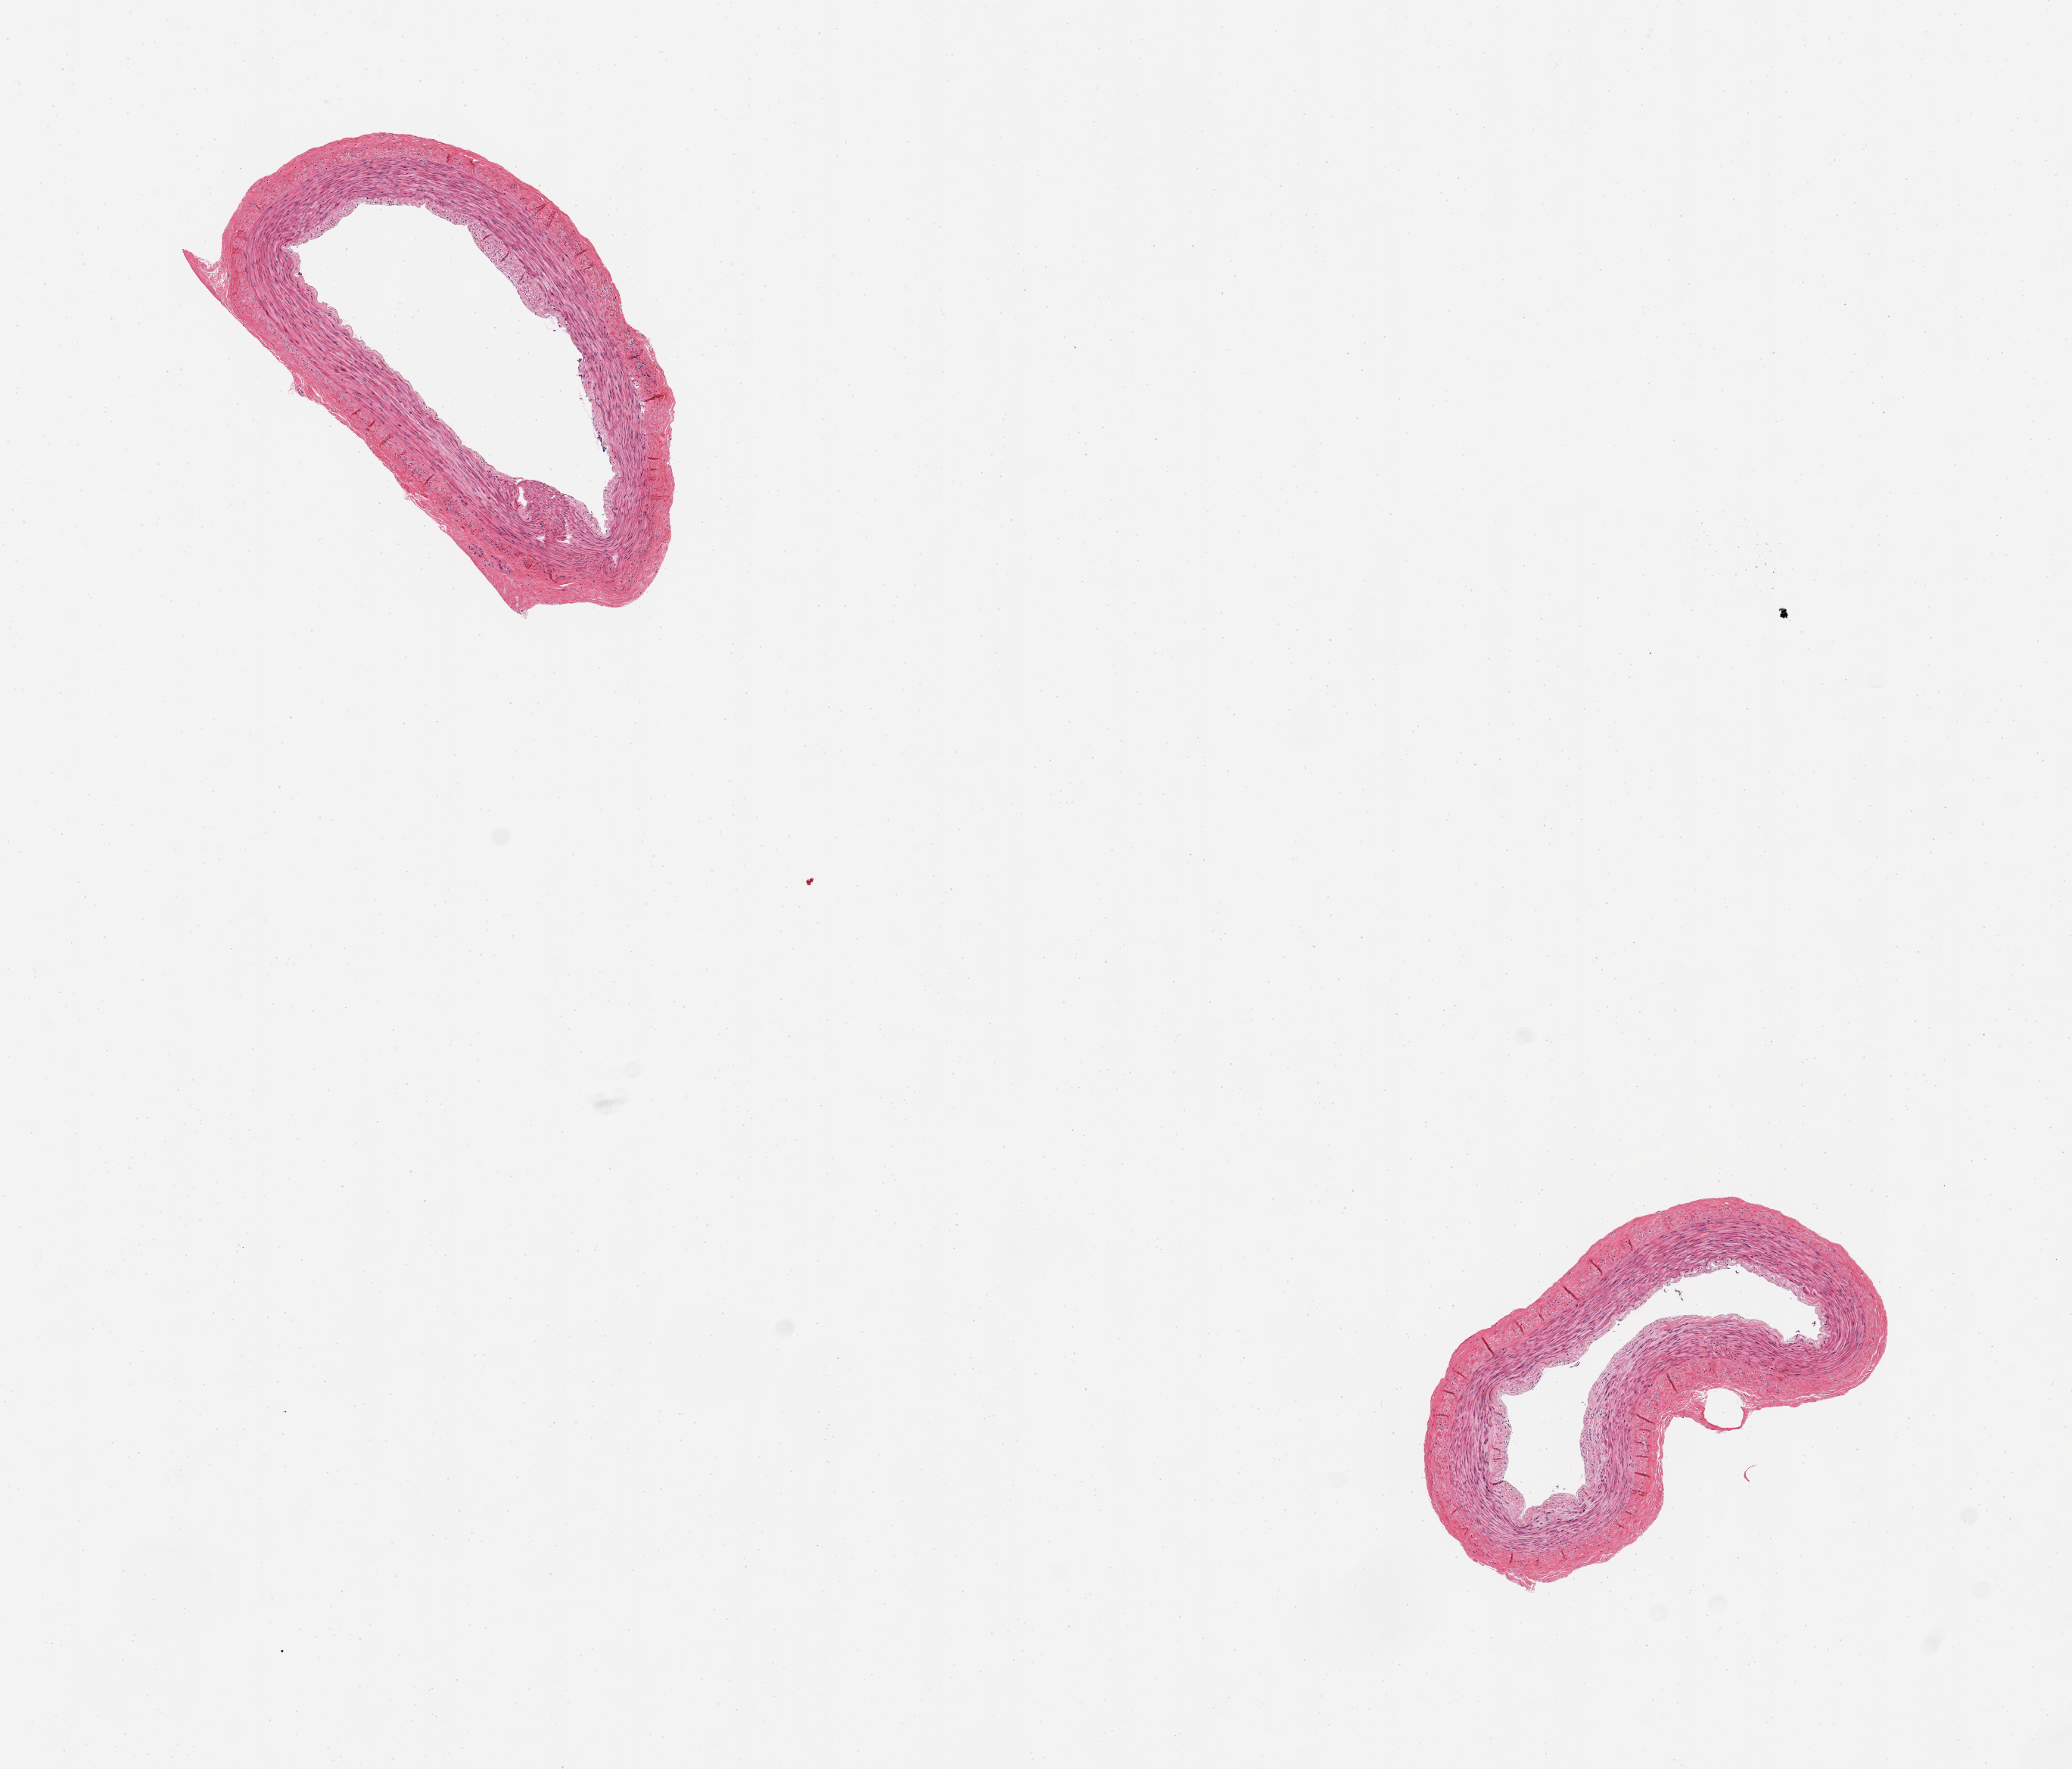
Whole-slide image, haematoxylin and eosin stain, whole scanned area (about 10.8 x 9.2 mm, from a 20x scan) shown as a low-resolution overview; PAXgene-fixed paraffin-embedded (PFPE) section; section of tibial artery (target tissue); donor tissue sample. Female donor.
Reviewer comment on this tissue sample: 2 pieces, no atherosis; good clean specimens, no adherent fat.